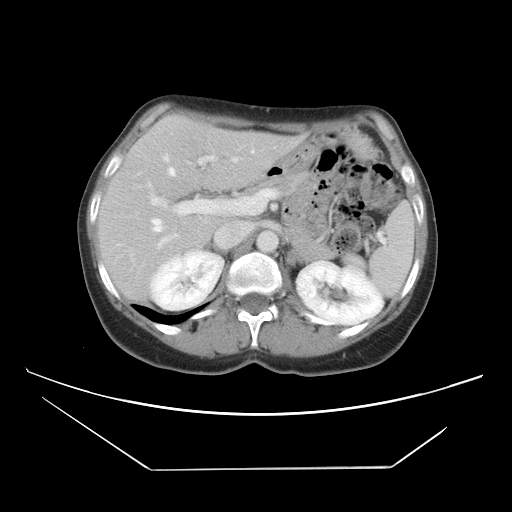
Contrast-enhanced abdominal CT, one axial slice. Position 27 of 42 along the scan axis. 120 kVp. Soft-tissue window (W 400 / L 40 HU). 512 × 512 image matrix, field of view 399 × 399 mm. Female patient, age 52 years. From the clinical record (not read from this slice): diagnosis: colorectal cancer liver metastases, imaged before liver resection; multiple liver metastases: yes; largest metastasis: 5.5 cm; chemotherapy before resection: yes.
Structures marked on this image (expert manual segmentation):
- hepatic veins: bounding box (x1, y1, x2, y2) in pixels: (138, 150, 254, 233)
- liver: (101, 118, 295, 300)
- planned liver remnant (the part of the liver to remain after resection): (114, 118, 219, 224)
- portal vein (with intrahepatic branches): (148, 145, 279, 245)